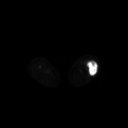
FDG PET of an extremity soft-tissue mass (from a PET/CT study), one axial slice. Position 207 of 267 along the scan axis. 3.27 mm slice thickness. 128 × 128 image matrix. Female patient, age 62 years. Case-level facts recorded for this patient, not image findings: histological type: undifferentiated – high grade; grade: high; site of the primary tumour: left thigh.
Outlined on this slice (expert contour drawn on MRI and transferred to this co-registered scan by the dataset authors):
- gross tumour volume including surrounding oedema: box from (x=83, y=60) to (x=97, y=75) px
- gross tumour volume (mass): (x=87, y=60)–(x=97, y=75)